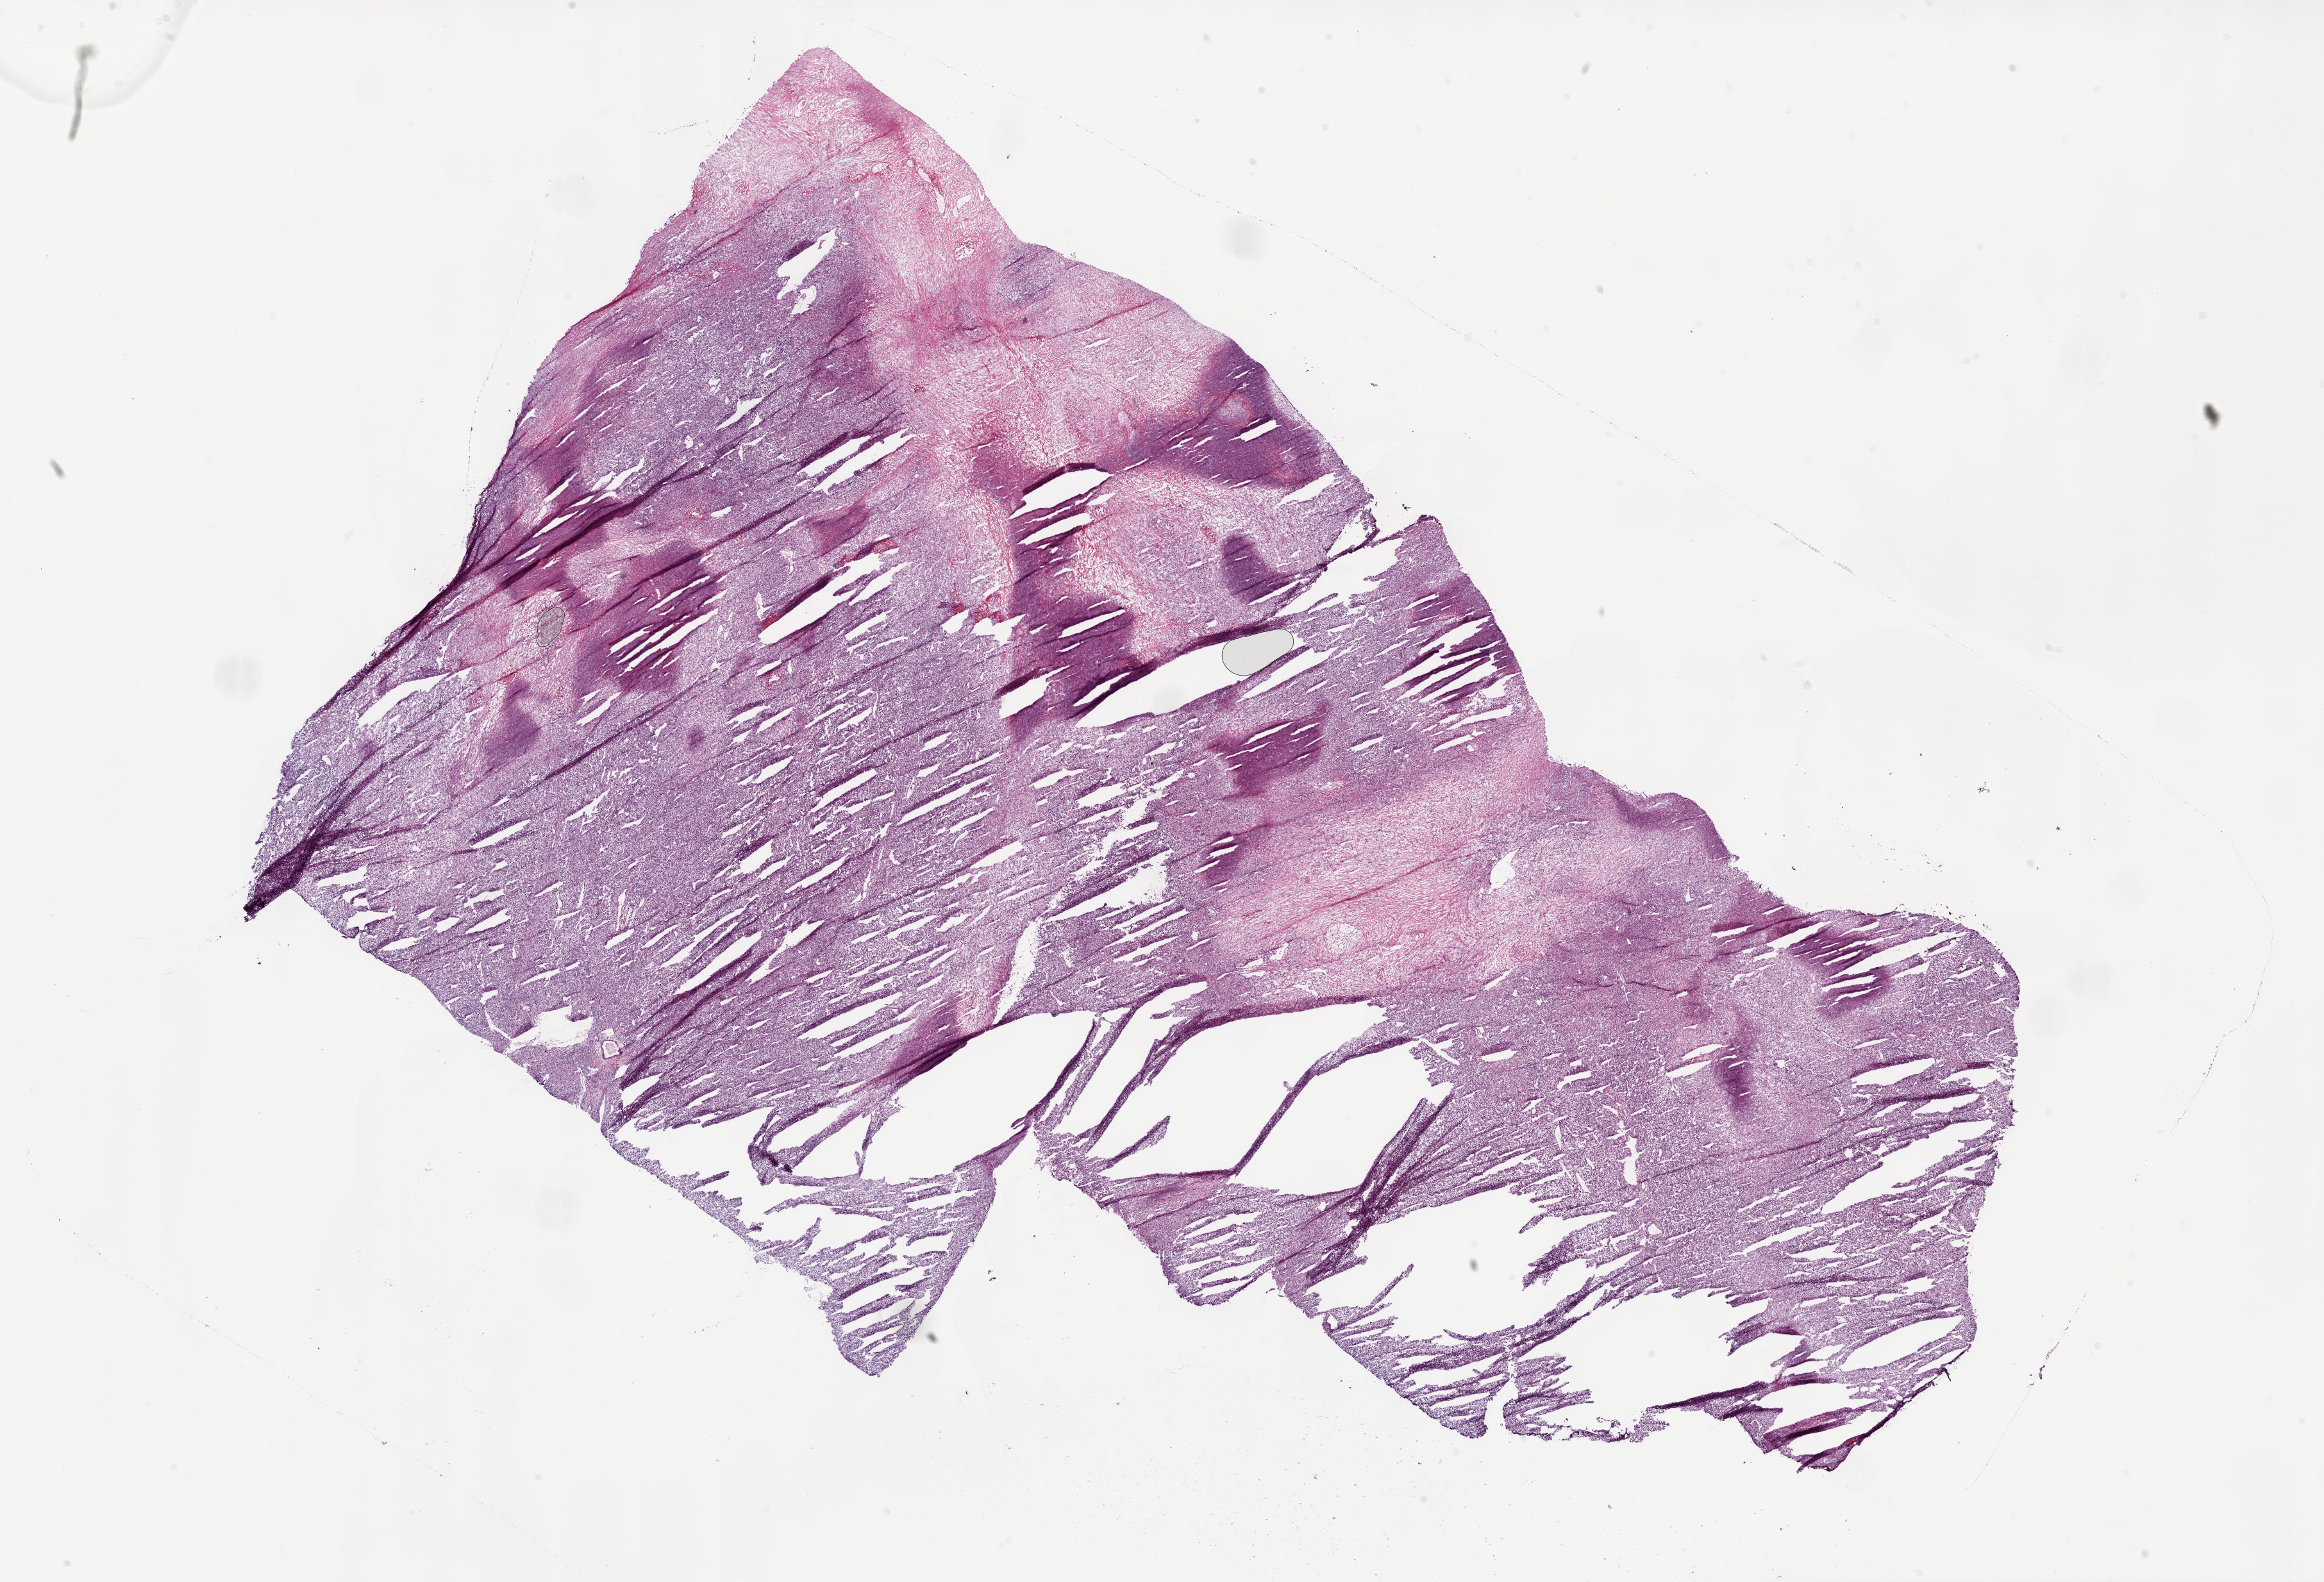
Digitized Hematoxylin and eosin (H&E) stained tissue section (whole slide) — a low-resolution overview of the entire scanned area, about 29.1 x 19.8 mm (from a 20x scan), frozen section from the bottom of the tissue portion, sample: primary tumour, kidney. Patient: male, age at initial diagnosis 40 years. Histologic grade: G4 (undifferentiated). Pathologist review of this section (percent, as recorded): tumour cells 70%, tumour nuclei 85%, normal cells 0%, stromal cells 20%, necrosis 10%.
- lymph nodes positive (case pathology): 1 of 21 examined
- pathologic diagnosis: Clear cell adenocarcinoma, NOS
- AJCC pathologic stage: IV